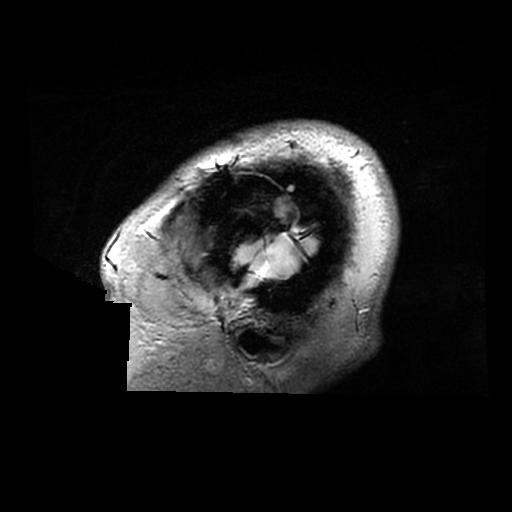
Brain MRI from a brain-tumour surgery series, one sagittal slice; position 262 of 320 along the scan axis; 512 × 512 image matrix. From the clinical record (not read from this slice): histopathology: Astrocytoma; WHO grade: 2; IDH mutation: yes.
Structures marked on this image (outlined manually by an expert reader):
- tumour: bounding box (x1, y1, x2, y2) in pixels: (235, 235, 314, 278)